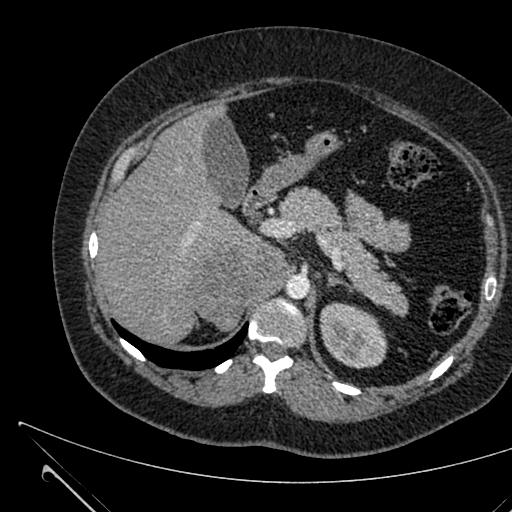
Contrast-enhanced abdominal CT, one axial slice. 120 kVp. Intravenous contrast given. Soft-tissue window (W 400 / L 40 HU). 1 mm slice thickness. 512 × 512 image matrix, field of view 376 × 376 mm. Female patient, age 36 years. From the clinical record (not read from this slice): diagnosis: adrenocortical carcinoma; tumour side: right adrenal; tumour size at pathology: 10 cm; Ki-67 index: 20 %; stage (as recorded): 4.
Structures marked on this image (semi-automatic segmentation, software-assisted and operator-edited):
- mass: bounding box <191,246,286,331> (left, top, right, bottom; pixels)